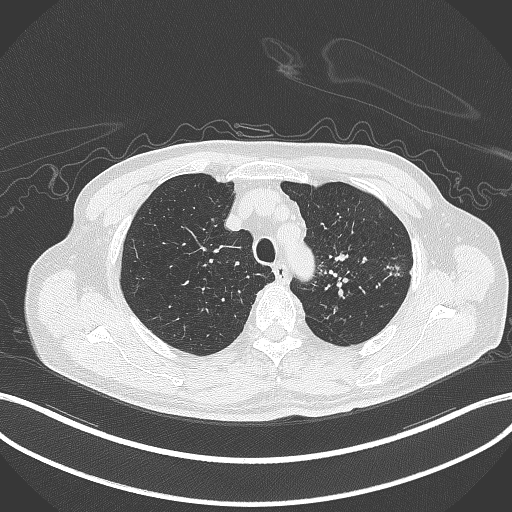
Chest CT, one axial slice. Position 351 of 417 along the scan axis. Reconstruction kernel B70f. 120 kVp. Lung window (W 1500 / L -600 HU). 1 mm slice thickness. 512 × 512 image matrix, field of view 400 × 400 mm. Patient: male, 77 years. Case-level facts recorded for this patient, not image findings: clinical TNM (as recorded): T3 N1 M0.
Structures marked on this image (rectangle marked by the reading radiologist):
- lung tumour (recorded histology: adenocarcinoma): box from (x=383, y=263) to (x=405, y=279) px